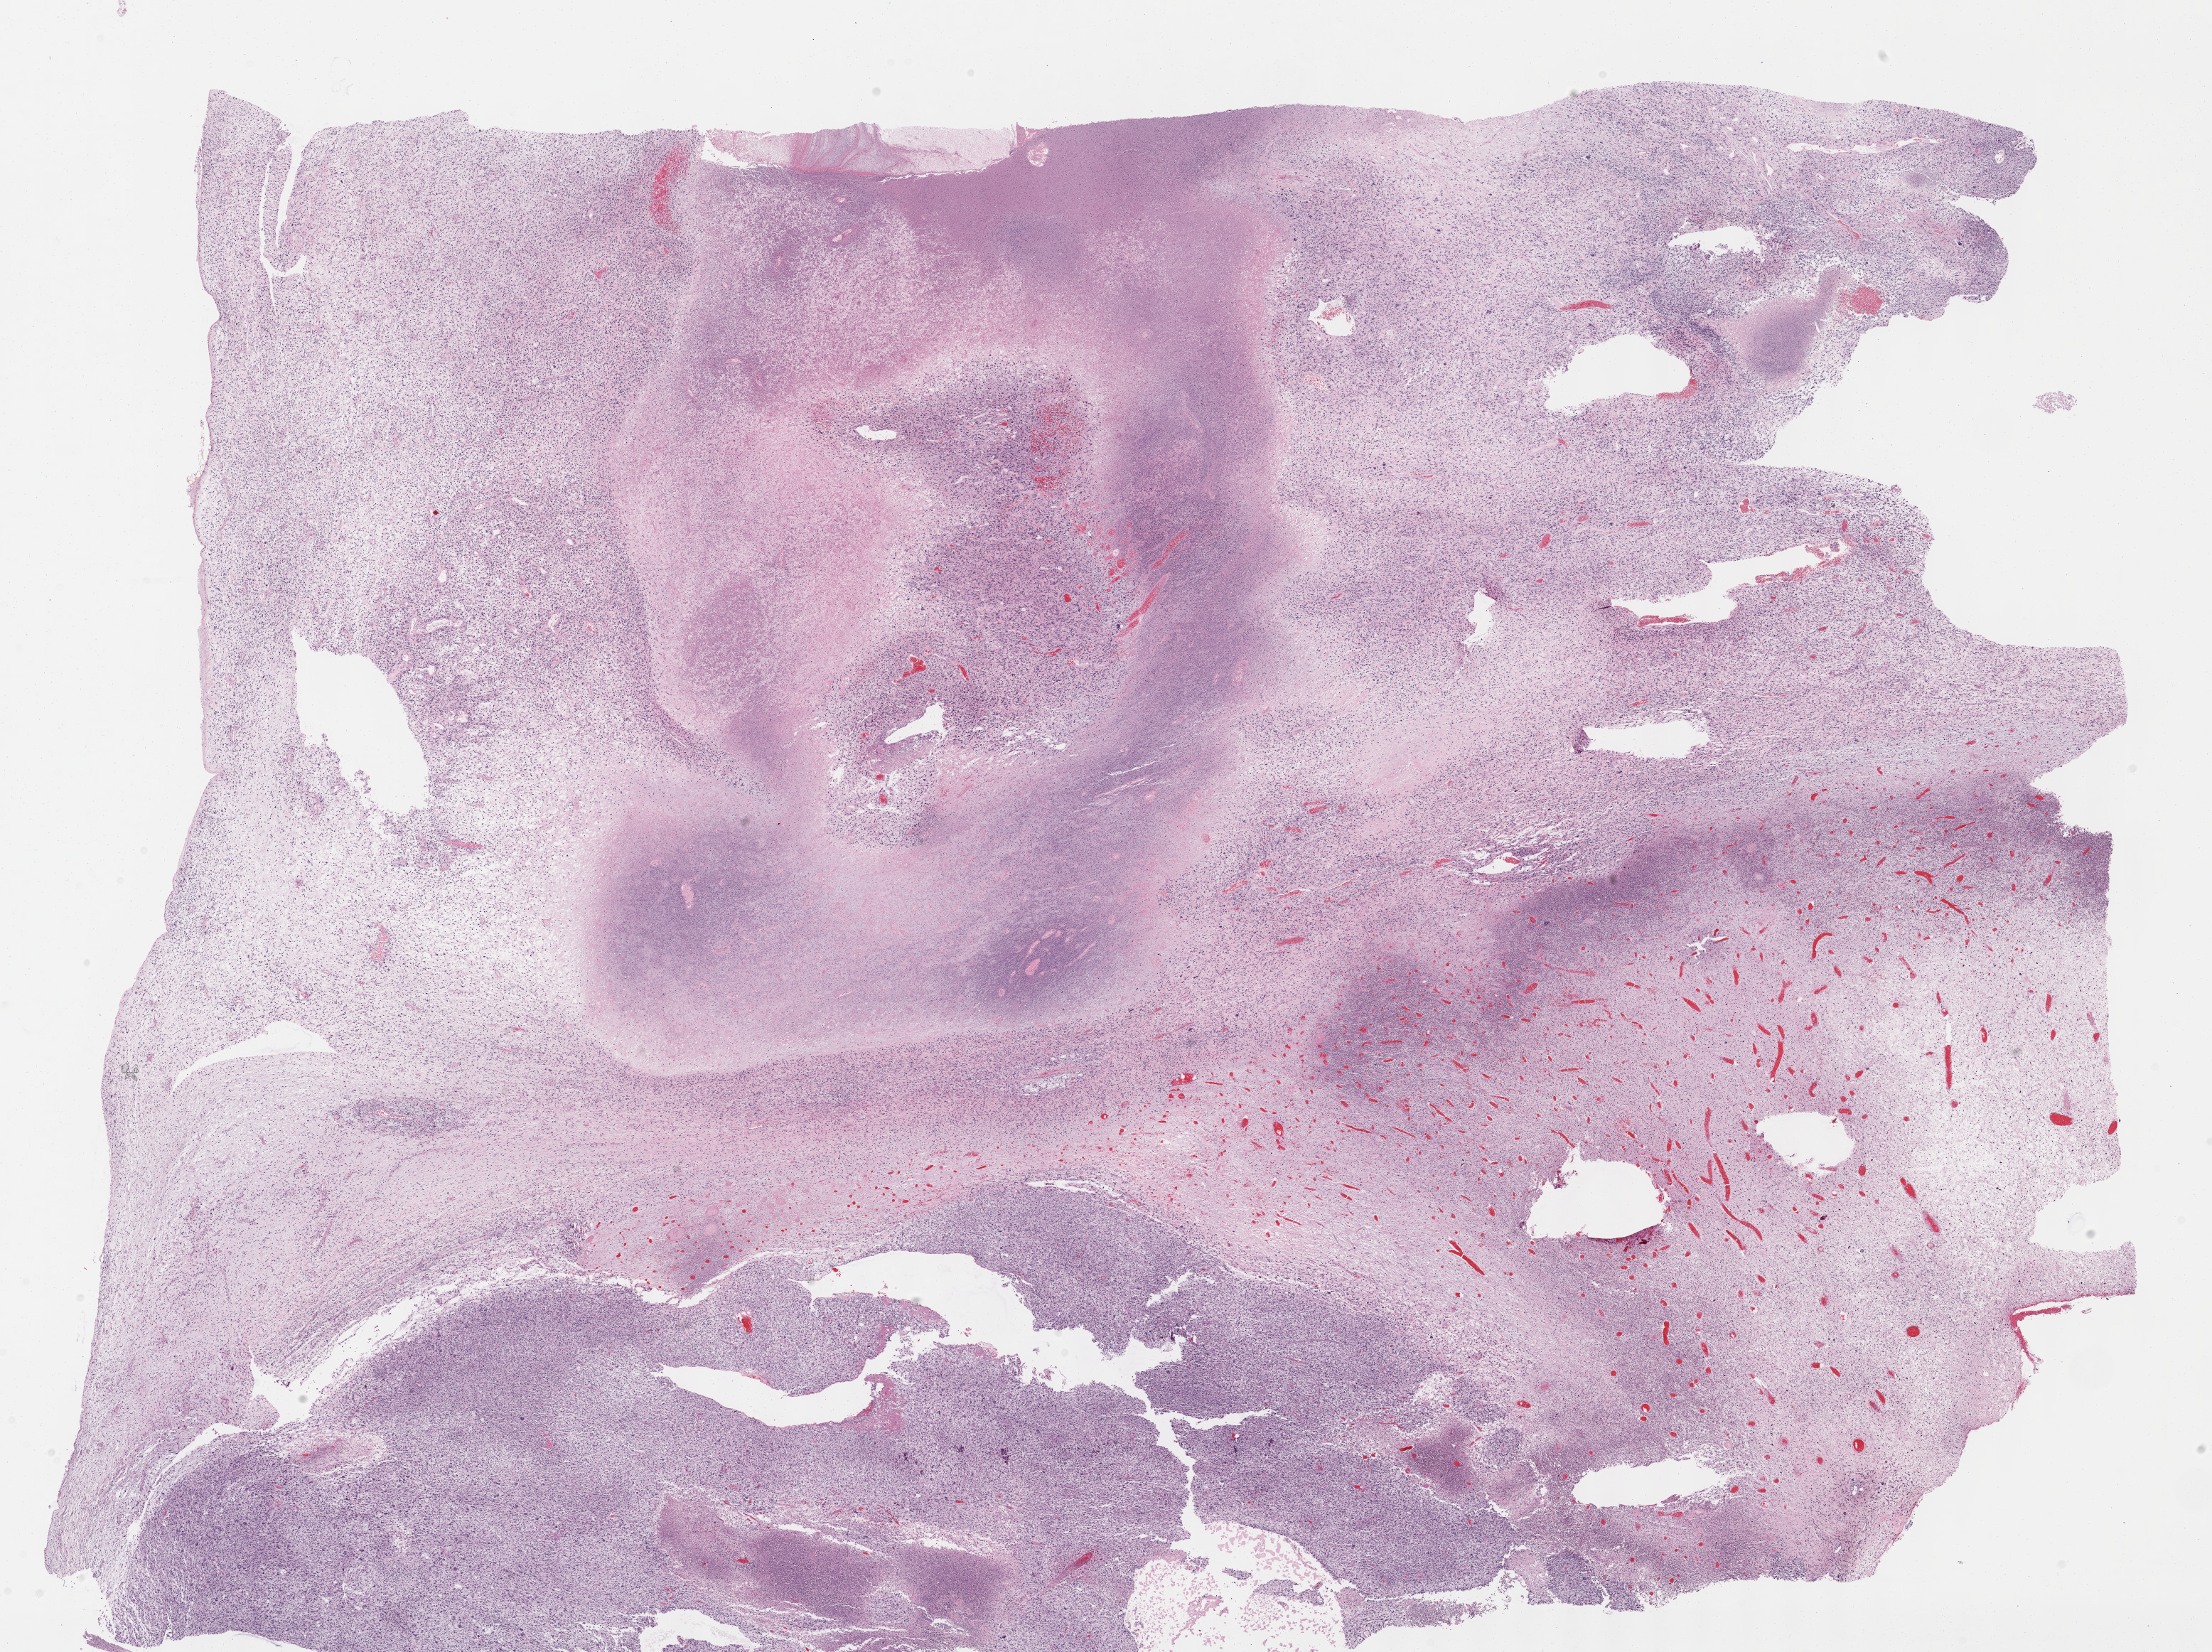
Whole-slide histology image, Hematoxylin and eosin (H&E) stained, whole scanned area (about 25.1 x 18.8 mm) shown as a low-resolution overview; formalin-fixed paraffin-embedded (FFPE) diagnostic section; primary tumour sample from the connective, subcutaneous and other soft tissues. Patient: female, age at initial diagnosis 83 years.
Diagnosis: Fibromyxosarcoma.